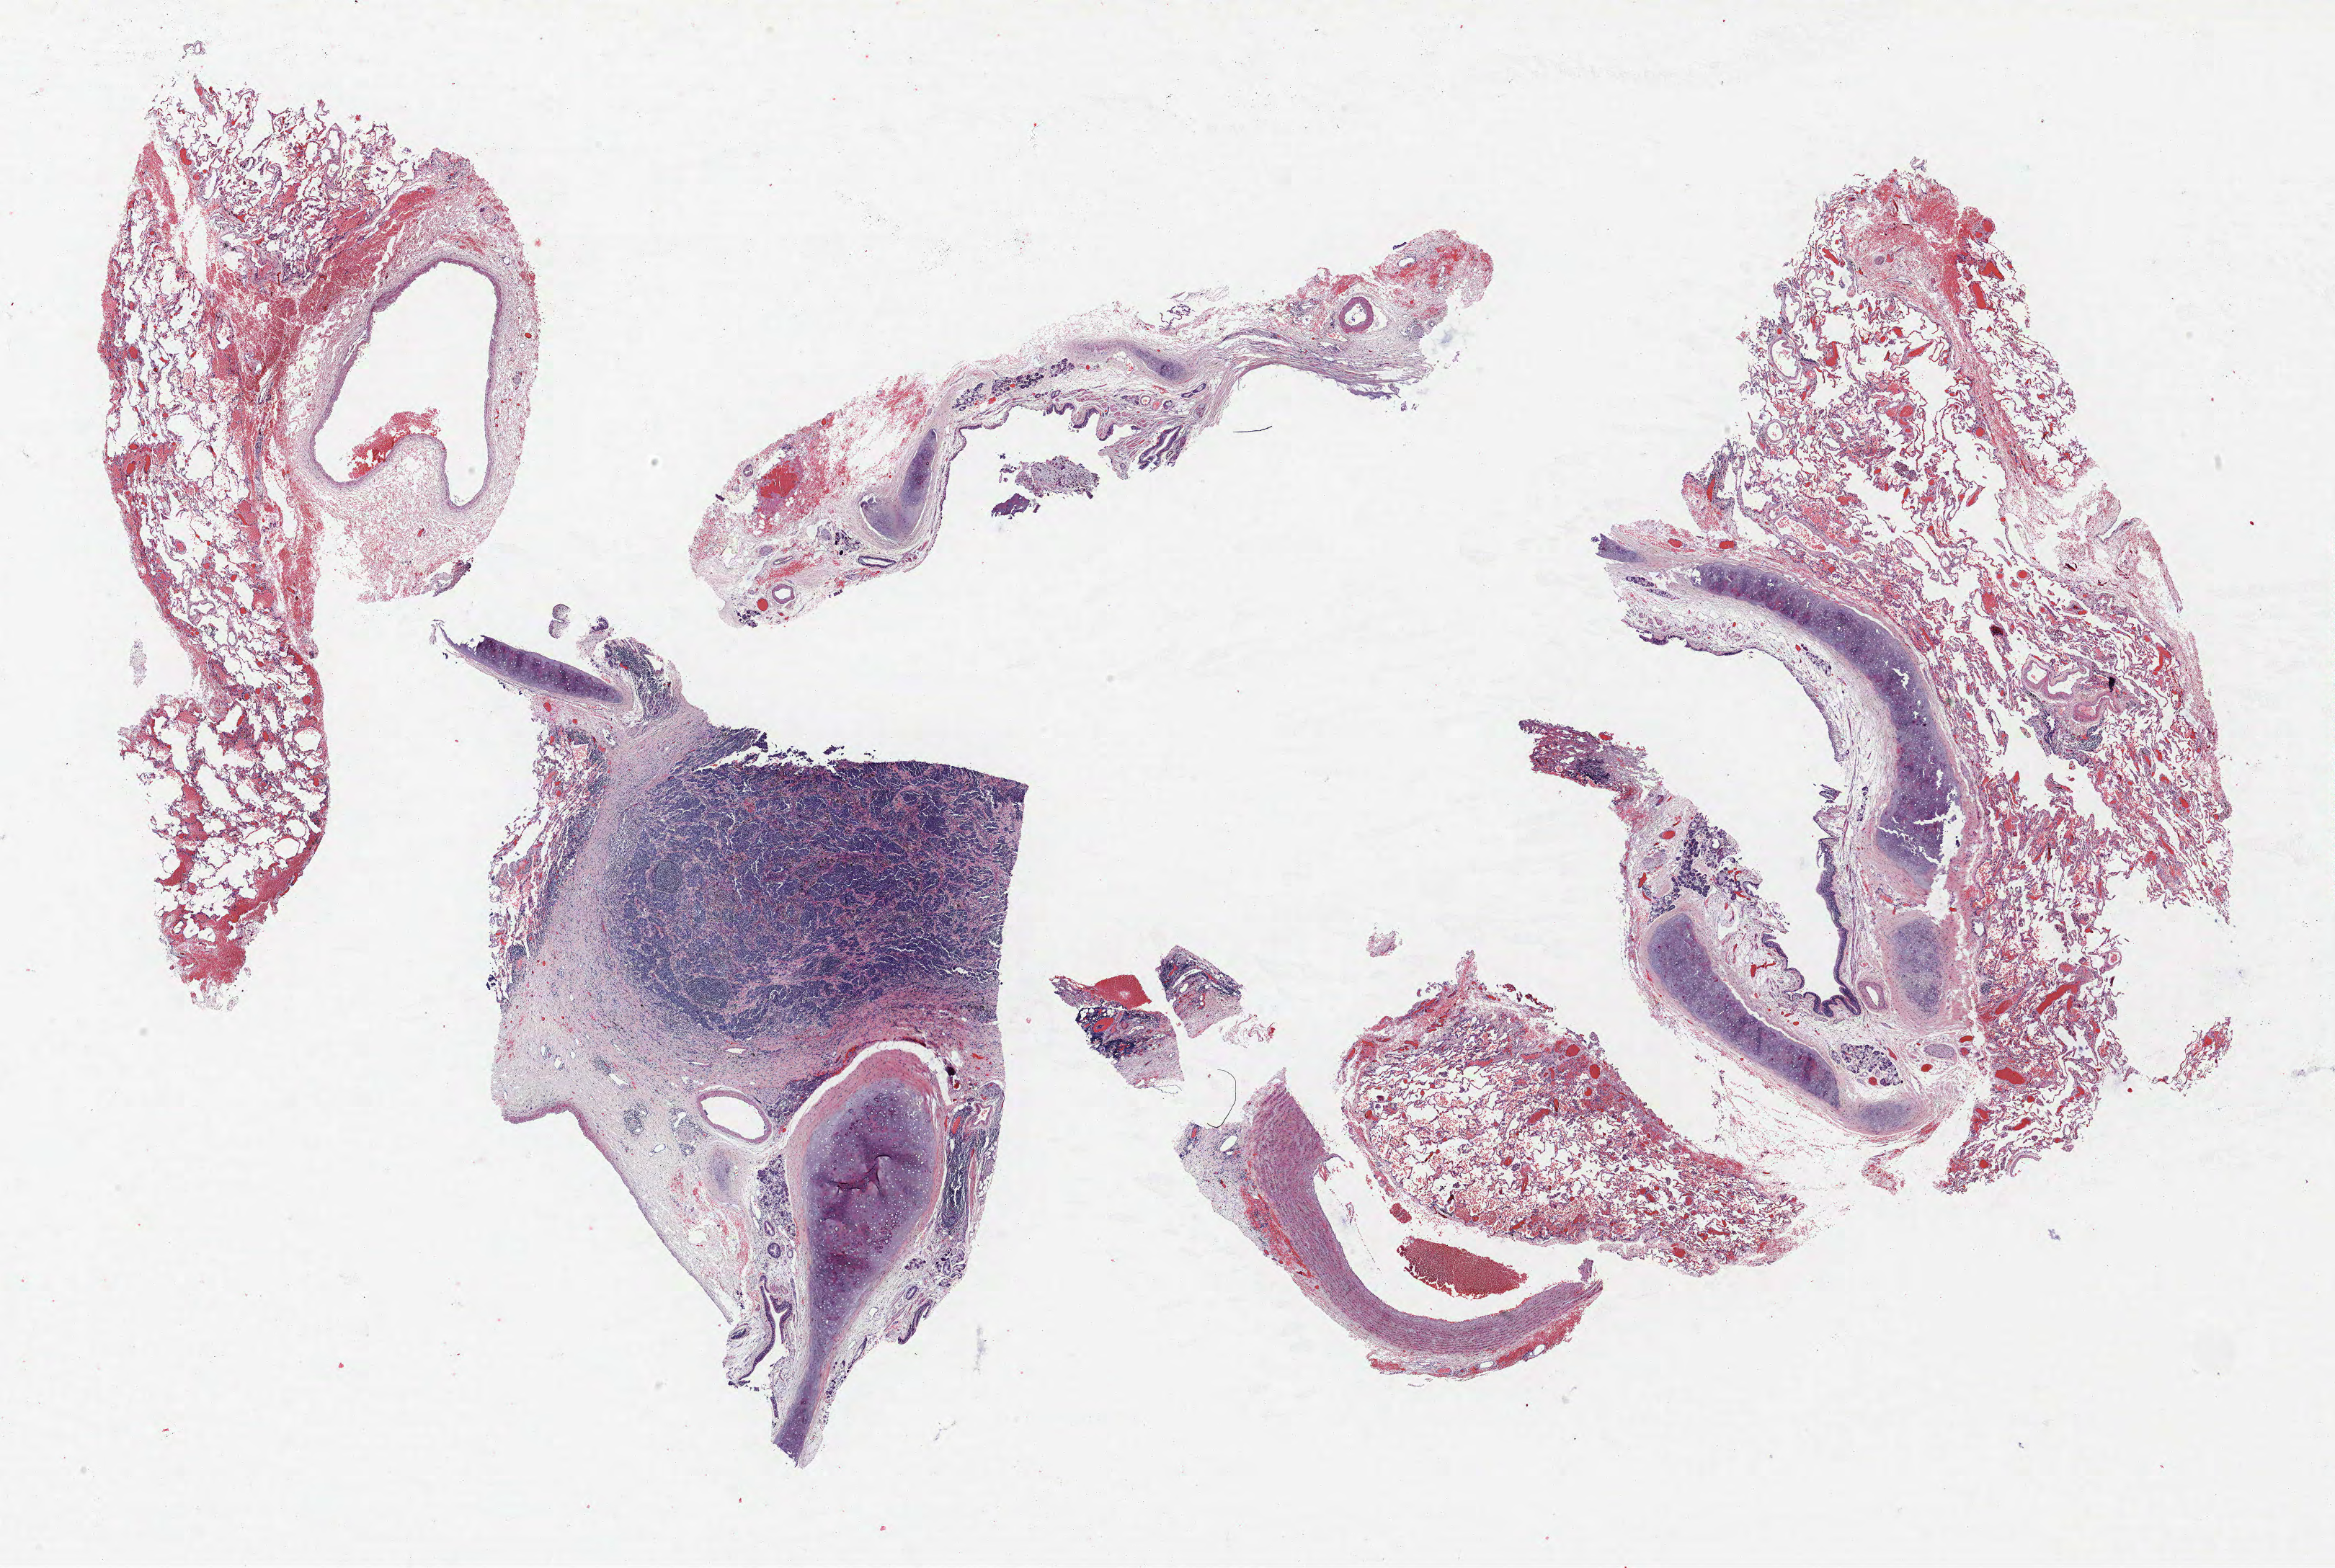
Whole-slide histology image, Hematoxylin and eosin (H&E) stained, whole scanned area (about 25.9 x 17.4 mm) shown as a low-resolution overview. Formalin-fixed paraffin-embedded (FFPE) section. Lung. Female, age 55 at enrolment. Current smoker at enrolment.
Tumour size (pathology): 24 mm. Stage (AJCC 6th edition): IIB. Participant's lung-cancer diagnosis: Small cell carcinoma, NOS (ICD-O-3 8041/3). ICD-O-3 topography: middle lobe of lung (C34.2). Primary tumour location (clinical record): right middle lobe.